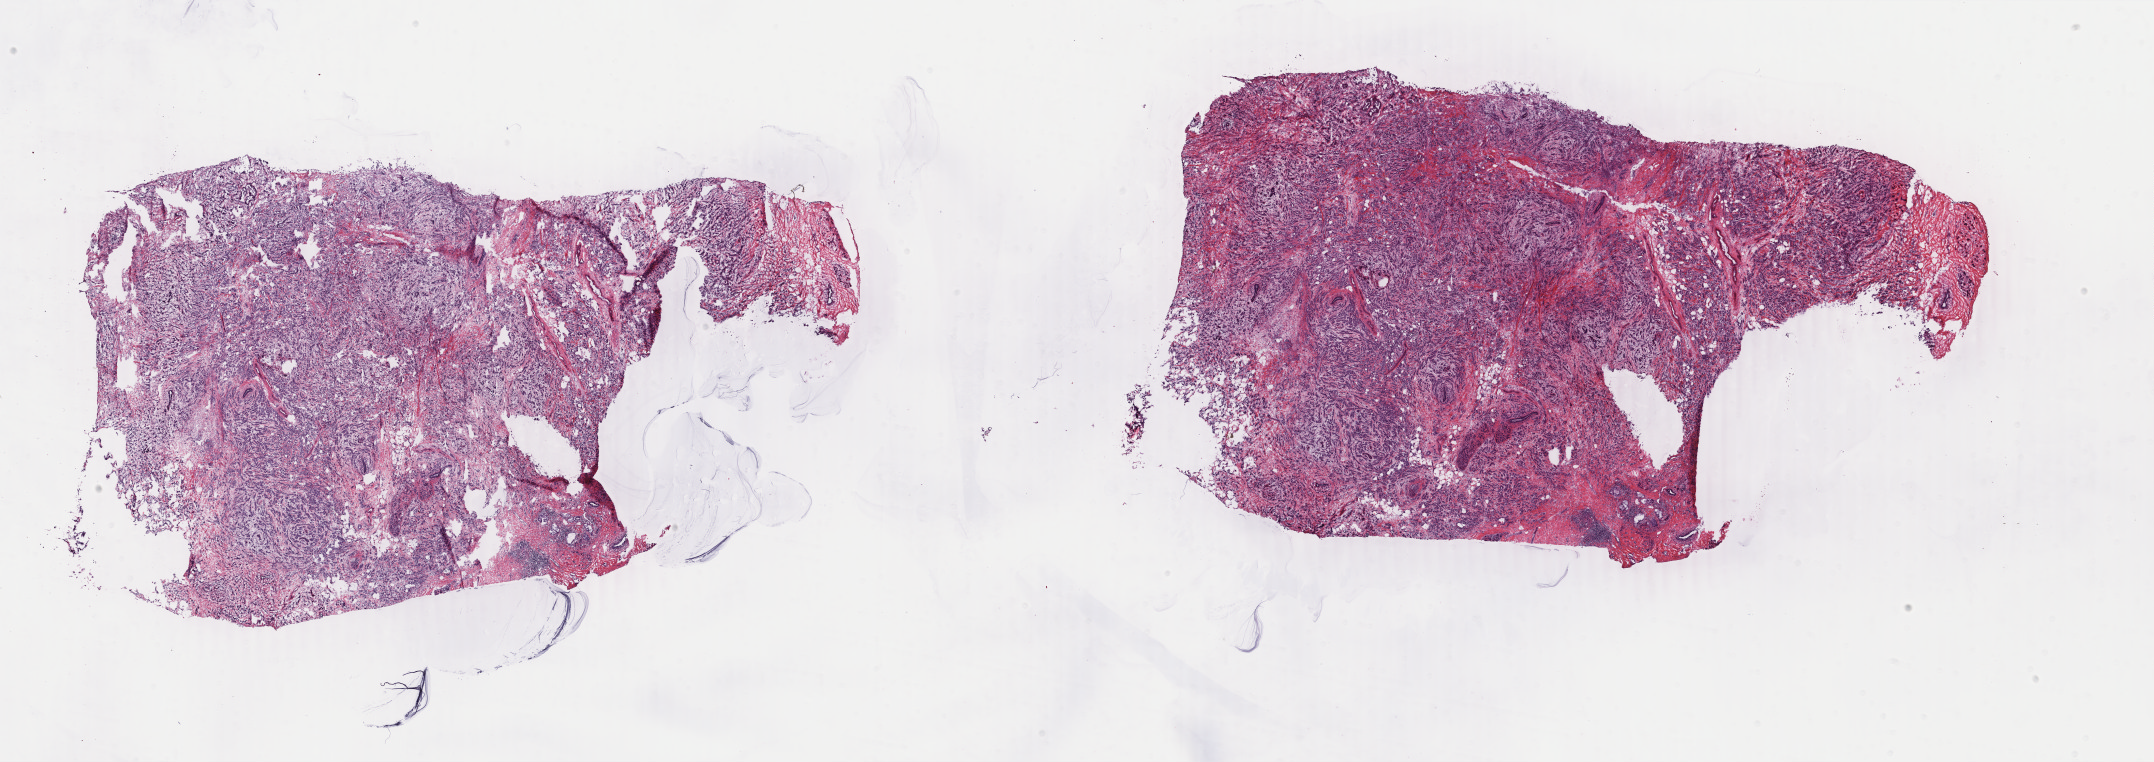
Digitized H&E tissue section (whole slide) — whole scanned area (about 34.3 x 12.1 mm) shown as a low-resolution overview. Frozen section from the top of the tissue portion. Breast, primary tumour sample. Female patient; age at initial diagnosis 36 years. Pathologist review of this section (percent, as recorded): tumour cells 80%, tumour nuclei 80%.
Diagnosis: Infiltrating duct carcinoma, NOS.